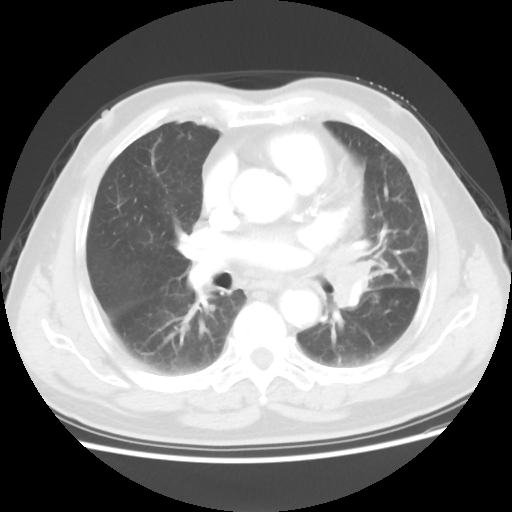
Chest CT, one axial slice; position 31 of 56 along the scan axis; 120 kVp; lung window (W 1500 / L -600 HU); 5 mm slice thickness; 512 × 512 image matrix. Male patient, age 75 years. From the clinical record (not read from this slice): clinical TNM (as recorded): T3 N0 M0.
Annotated regions visible in this slice (rectangle marked by the reading radiologist):
- lung tumour (recorded histology: squamous cell carcinoma): bounding box [x1, y1, x2, y2] px = [326, 242, 384, 317]